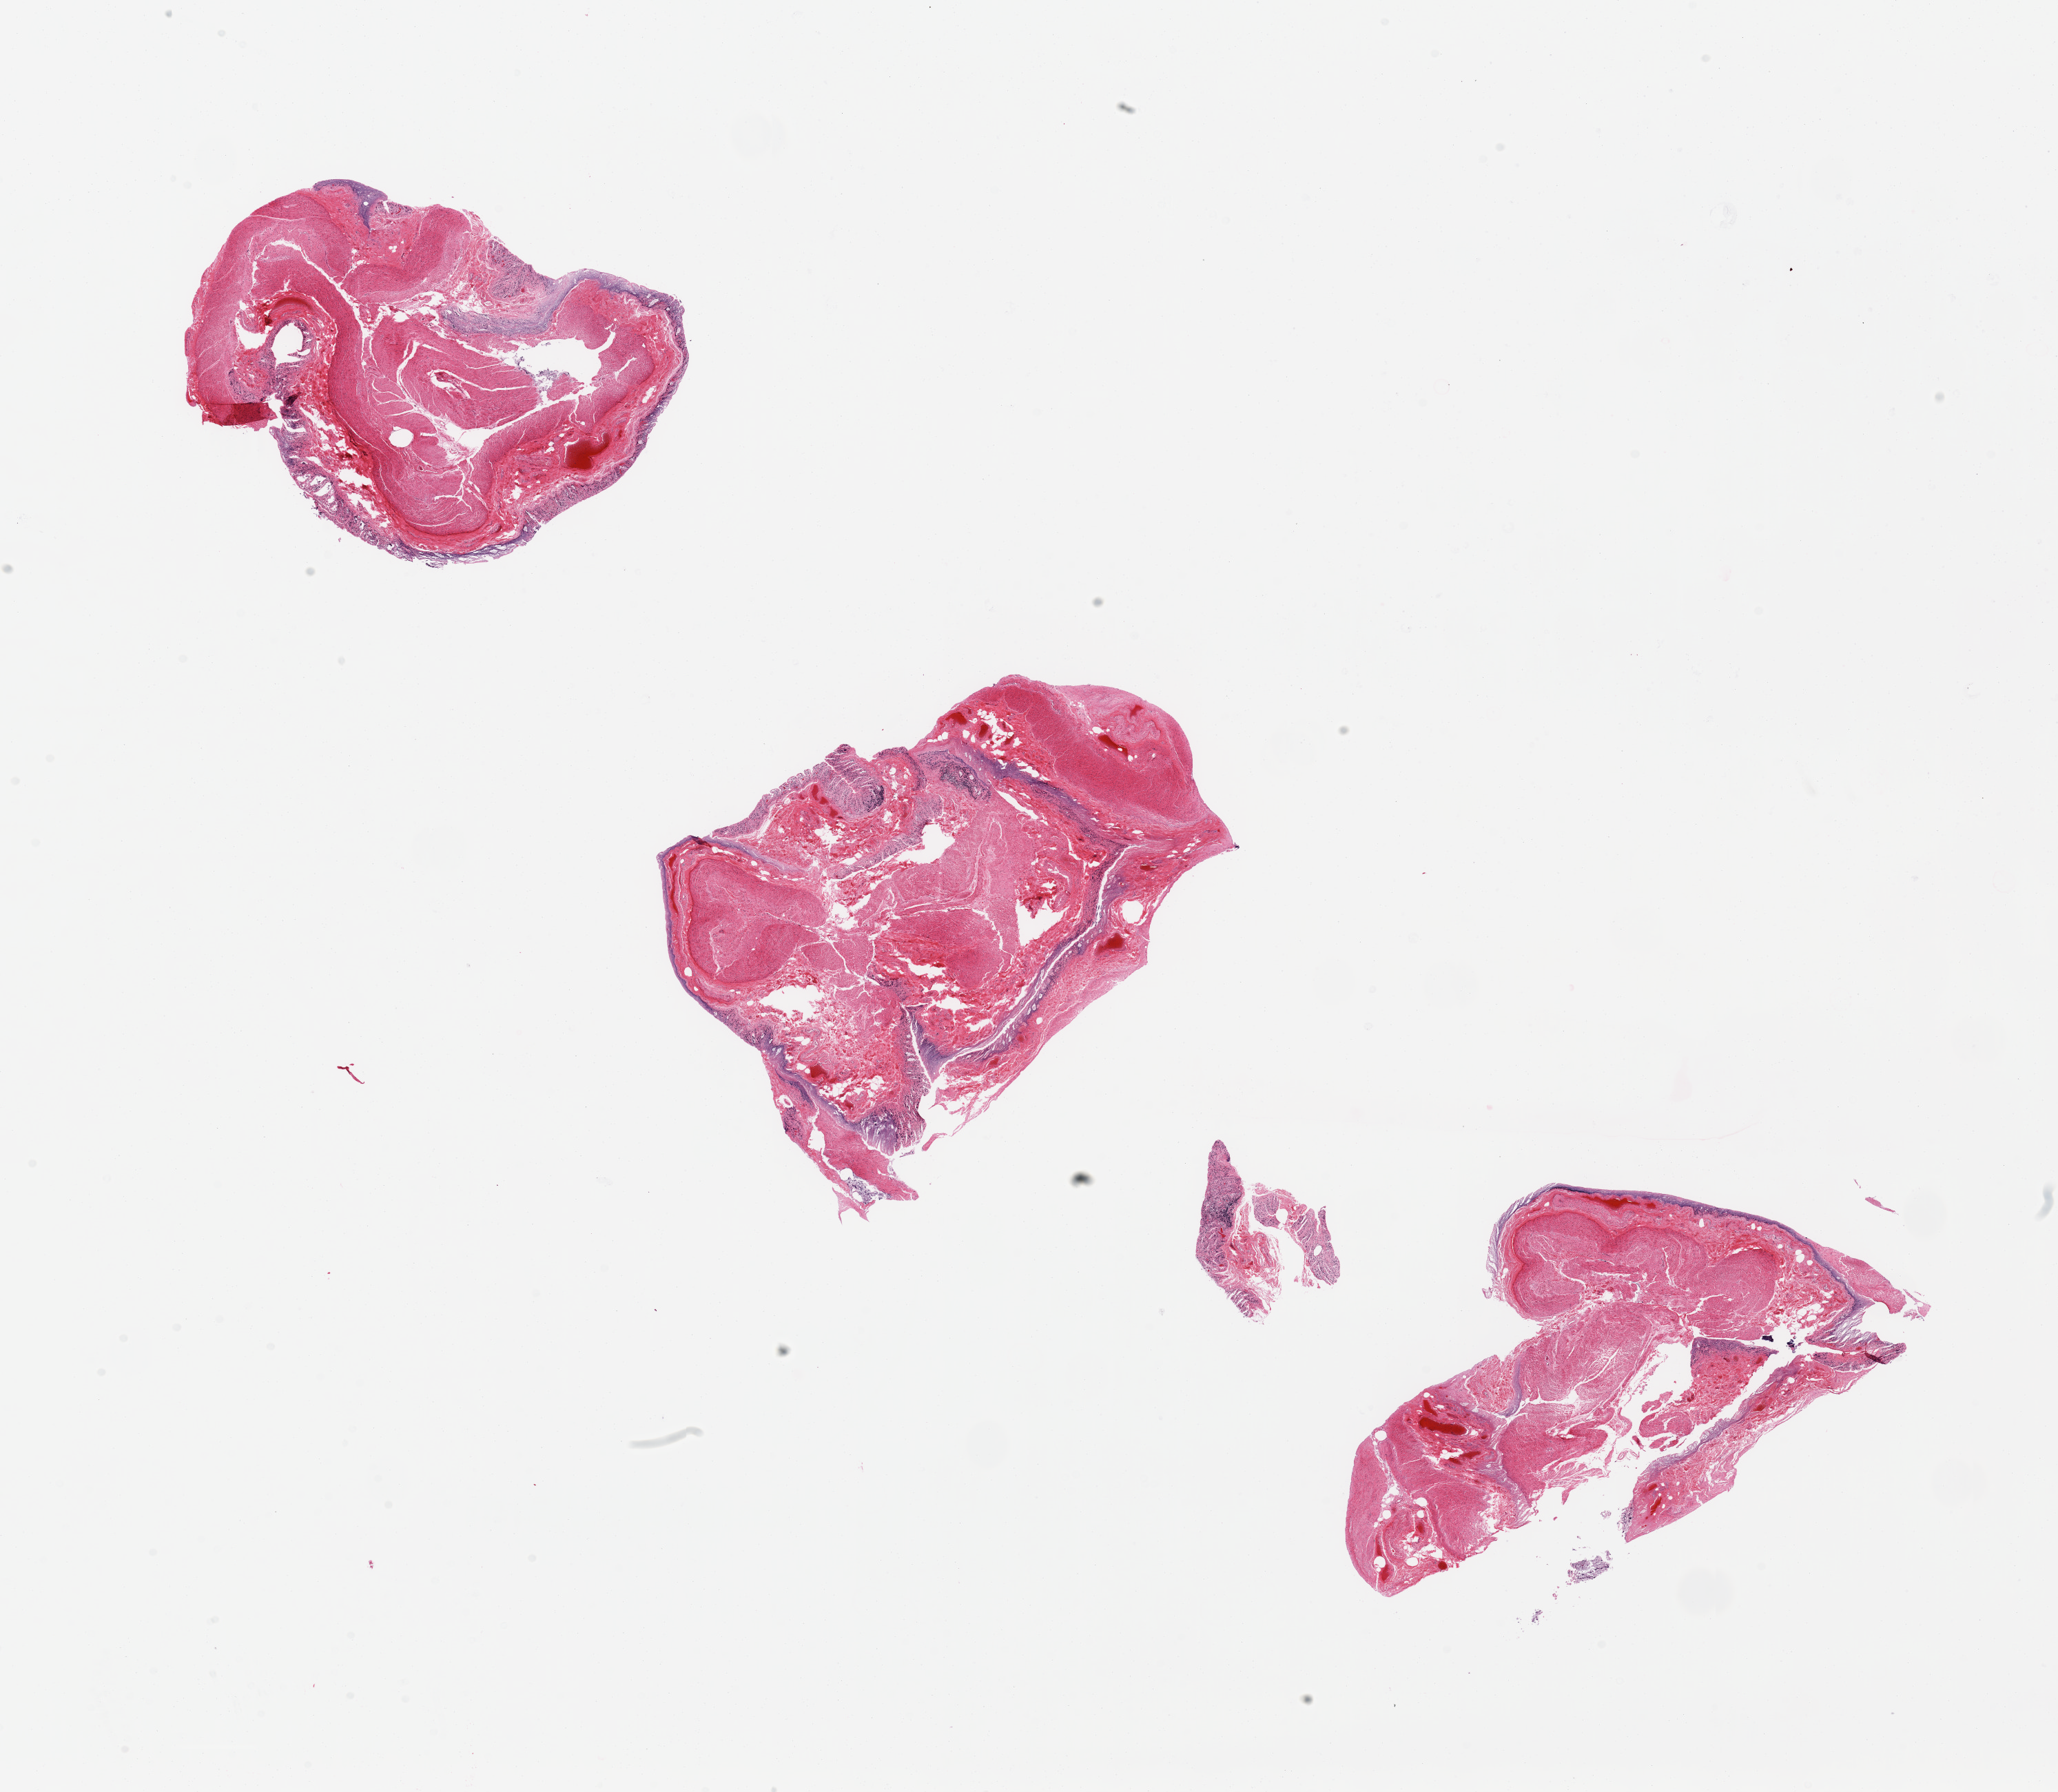
Whole-slide image, hematoxylin and eosin (H&E) stain, low-resolution overview of the scanned area, about 23.6 x 20.6 mm; PAXgene-fixed, paraffin-embedded tissue; section of transverse colon (target tissue); donor tissue sample.
Reviewer comment on this tissue sample: Glands 100% autolyzed; remainder slightly autolyzed.